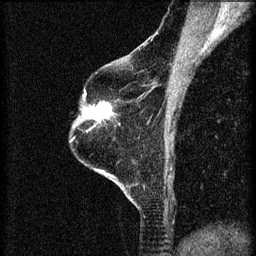
Breast MRI (dynamic contrast-enhanced), one sagittal slice; position 45 of 60 along the scan axis; 3 images stored at this slice position (order not interpretable as contrast timing); 1.5 T; TE 4.2 ms, TR 8.2 ms; 2 mm slice thickness; 256 × 256 image matrix, field of view 180 × 180 mm. Female patient, age 60 years.
Outlined on this slice (semi-automatic segmentation, software-assisted and operator-edited):
- analysis volume of interest (the breast-tissue region the enhancement analysis was run in; not a lesion): bounding box [x1, y1, x2, y2] px = [78, 94, 112, 125]
- tumour enhancement mask (voxels above the 70 % enhancement threshold inside the analysis volume of interest): [83, 94, 111, 121]